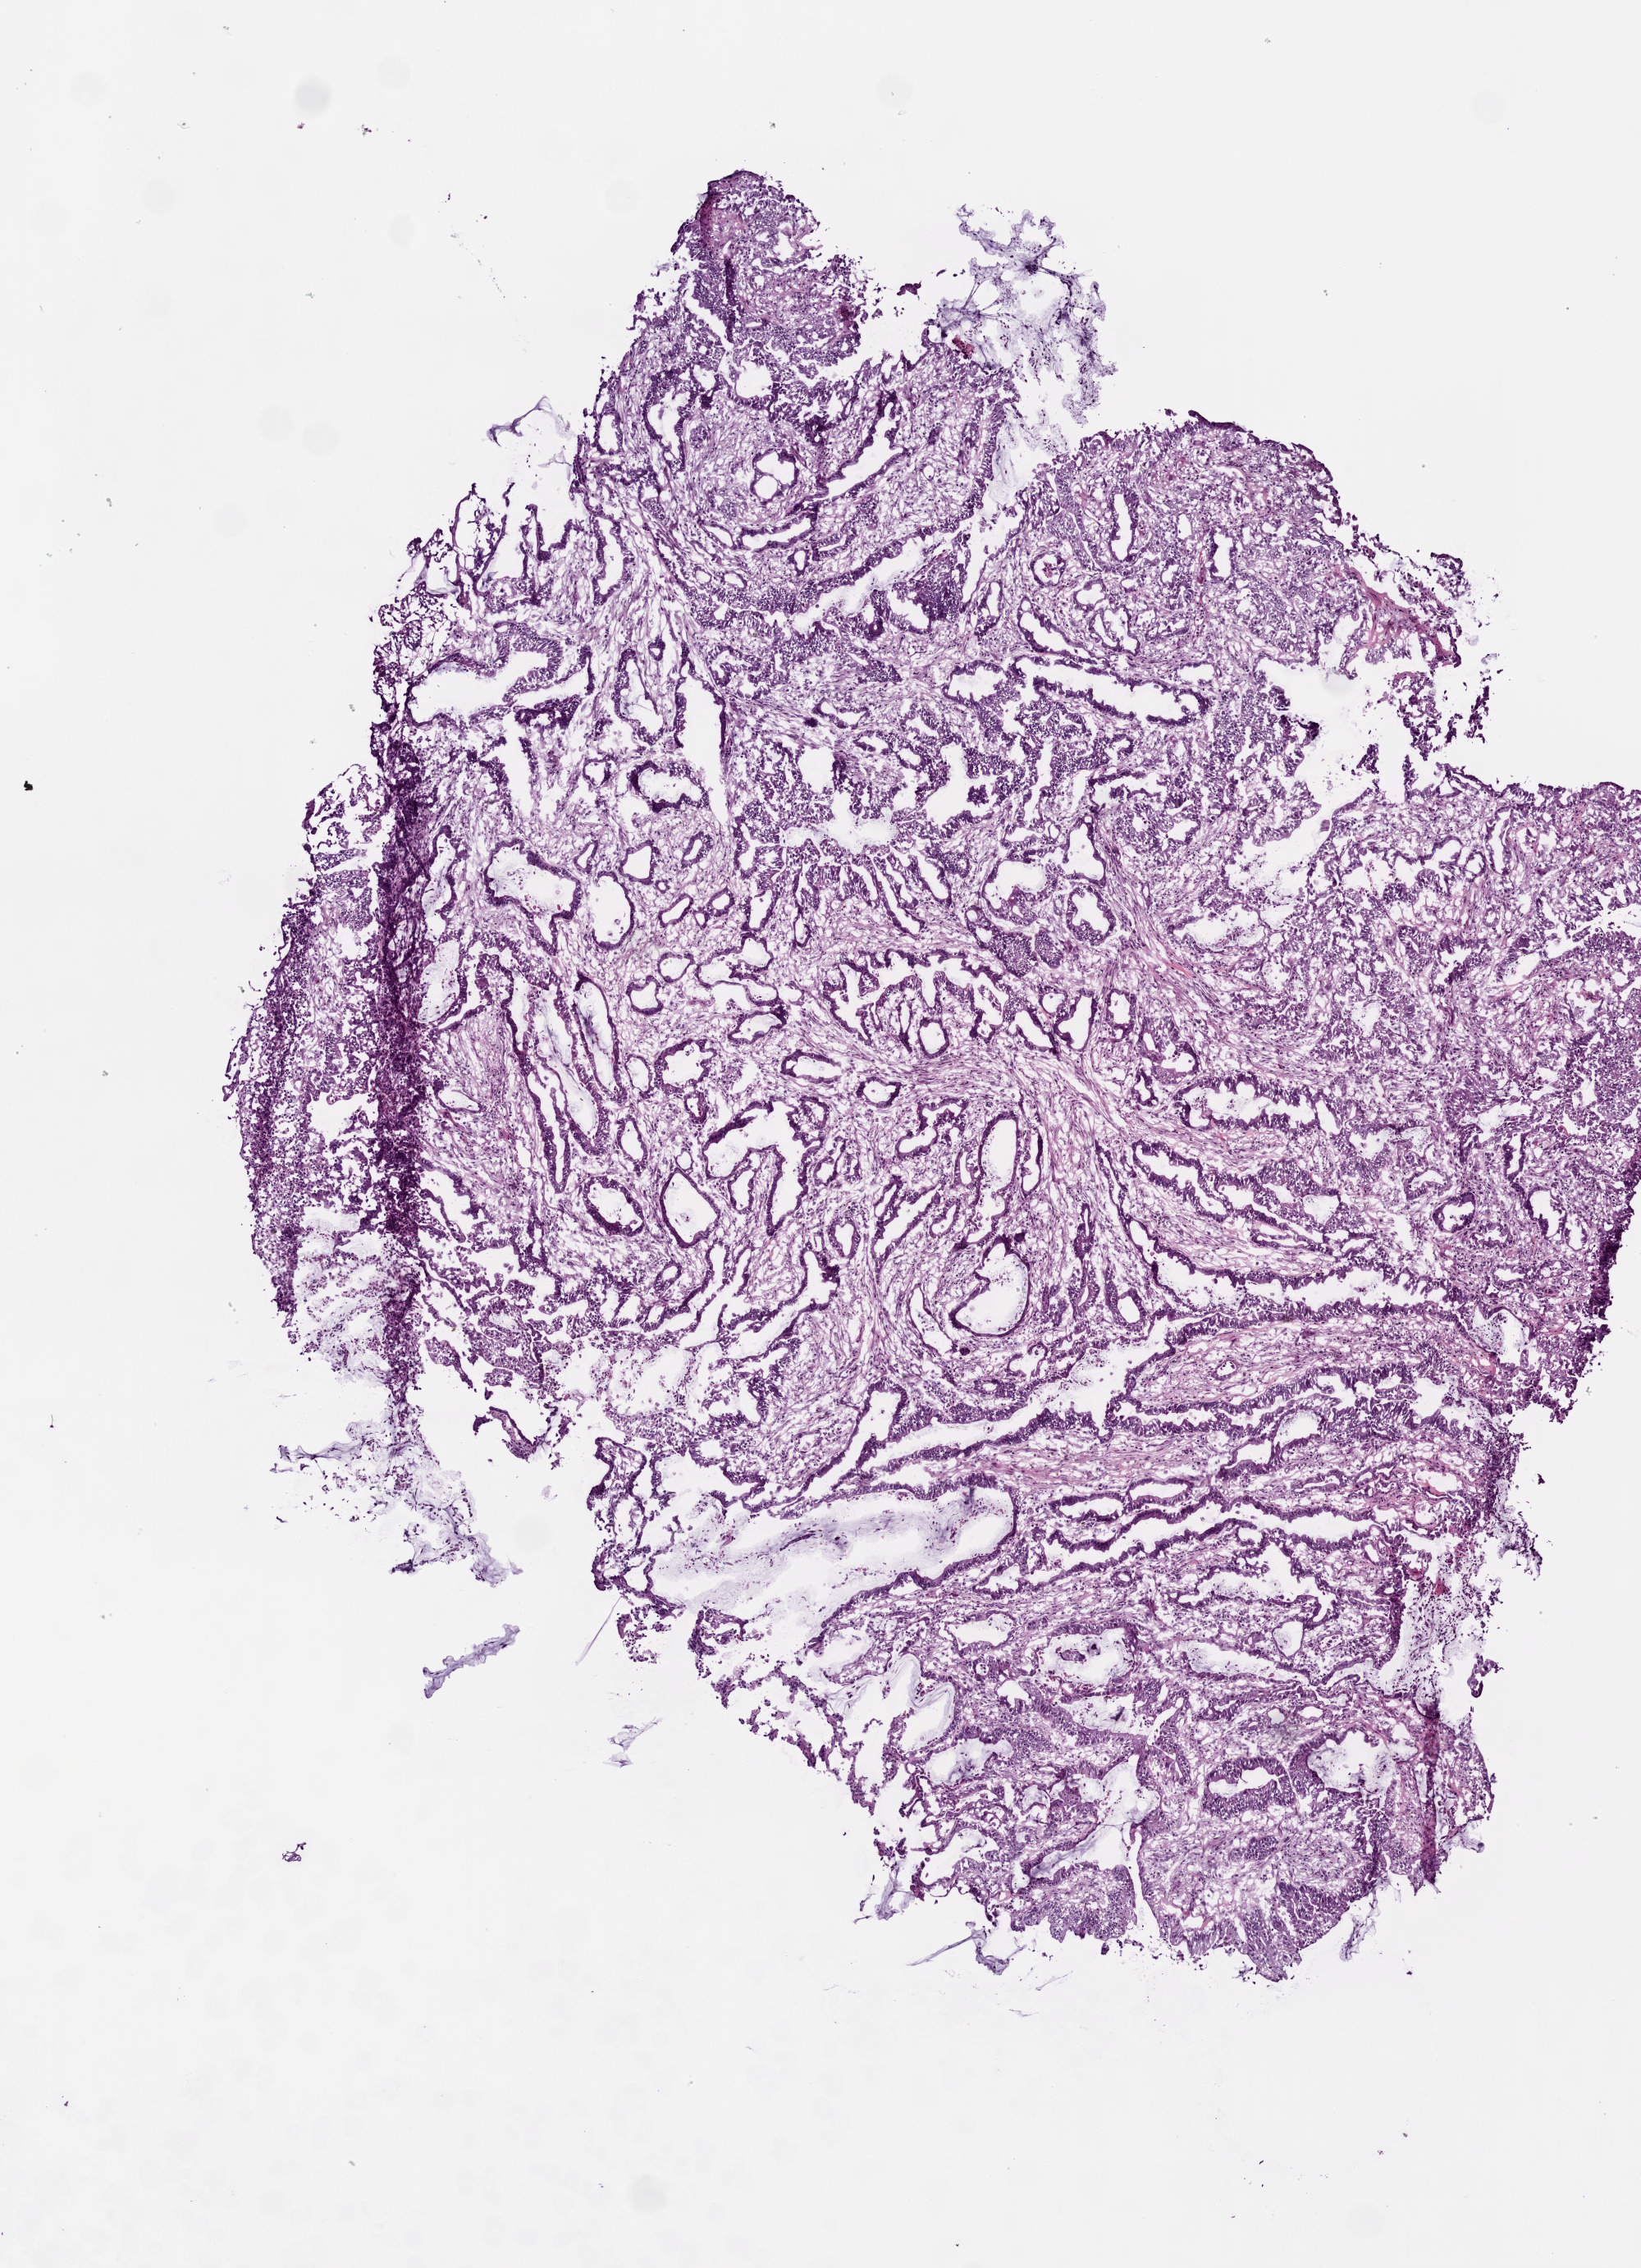
Digitized Hematoxylin and eosin (H&E) stained tissue section (whole slide) — low-resolution overview of the scanned area, about 4.0 x 5.5 mm, frozen section from the bottom of the tissue portion, sample: primary tumour, colon. Female, age 79 years at initial diagnosis. Slide review estimates, as recorded: tumour cells 77%, tumour nuclei 75%, normal cells 3%, stromal cells 20%, necrosis 0%.
• AJCC pathologic stage: IIA (6th edition)
• diagnosis: Mucinous adenocarcinoma (cecum)